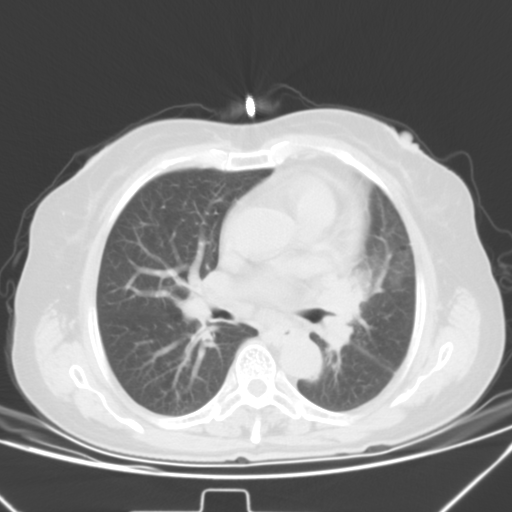
Chest CT, one axial slice. Lung window (W 1500 / L -600 HU). 5 mm slice thickness. 512 × 512 image matrix, field of view 331 × 331 mm. Female patient, age 59 years. From the clinical record (not read from this slice): clinical TNM (as recorded): T3 N1 M0; histopathological grade: G3.
Annotated regions visible in this slice (rectangle marked by the reading radiologist):
- lung tumour (recorded histology: small cell carcinoma): bounding box <316,268,374,355> (left, top, right, bottom; pixels)